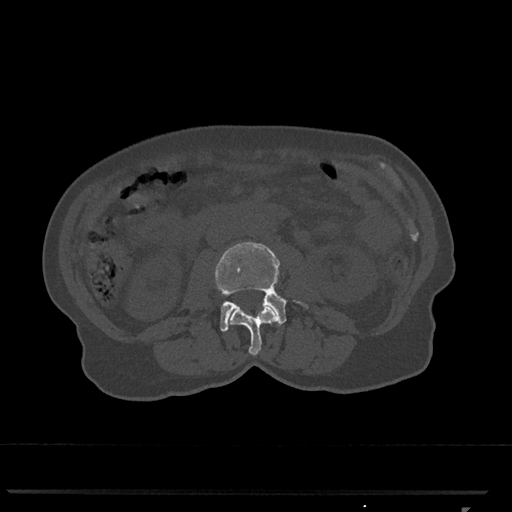
CT including the spine, one axial slice. Reconstruction kernel Br40s/3. 120 kVp. Bone window (W 1800 / L 400 HU). 0.5 mm slice thickness. 512 × 512 image matrix. Female patient, age 62 years. Case-level facts recorded for this patient, not image findings: primary cancer: renal.
Annotated regions visible in this slice (semi-automatic segmentation, software-assisted and operator-edited):
- L2 vertebra: box from (x=228, y=305) to (x=278, y=356) px
- L3 vertebra: (x=215, y=242)–(x=308, y=332)